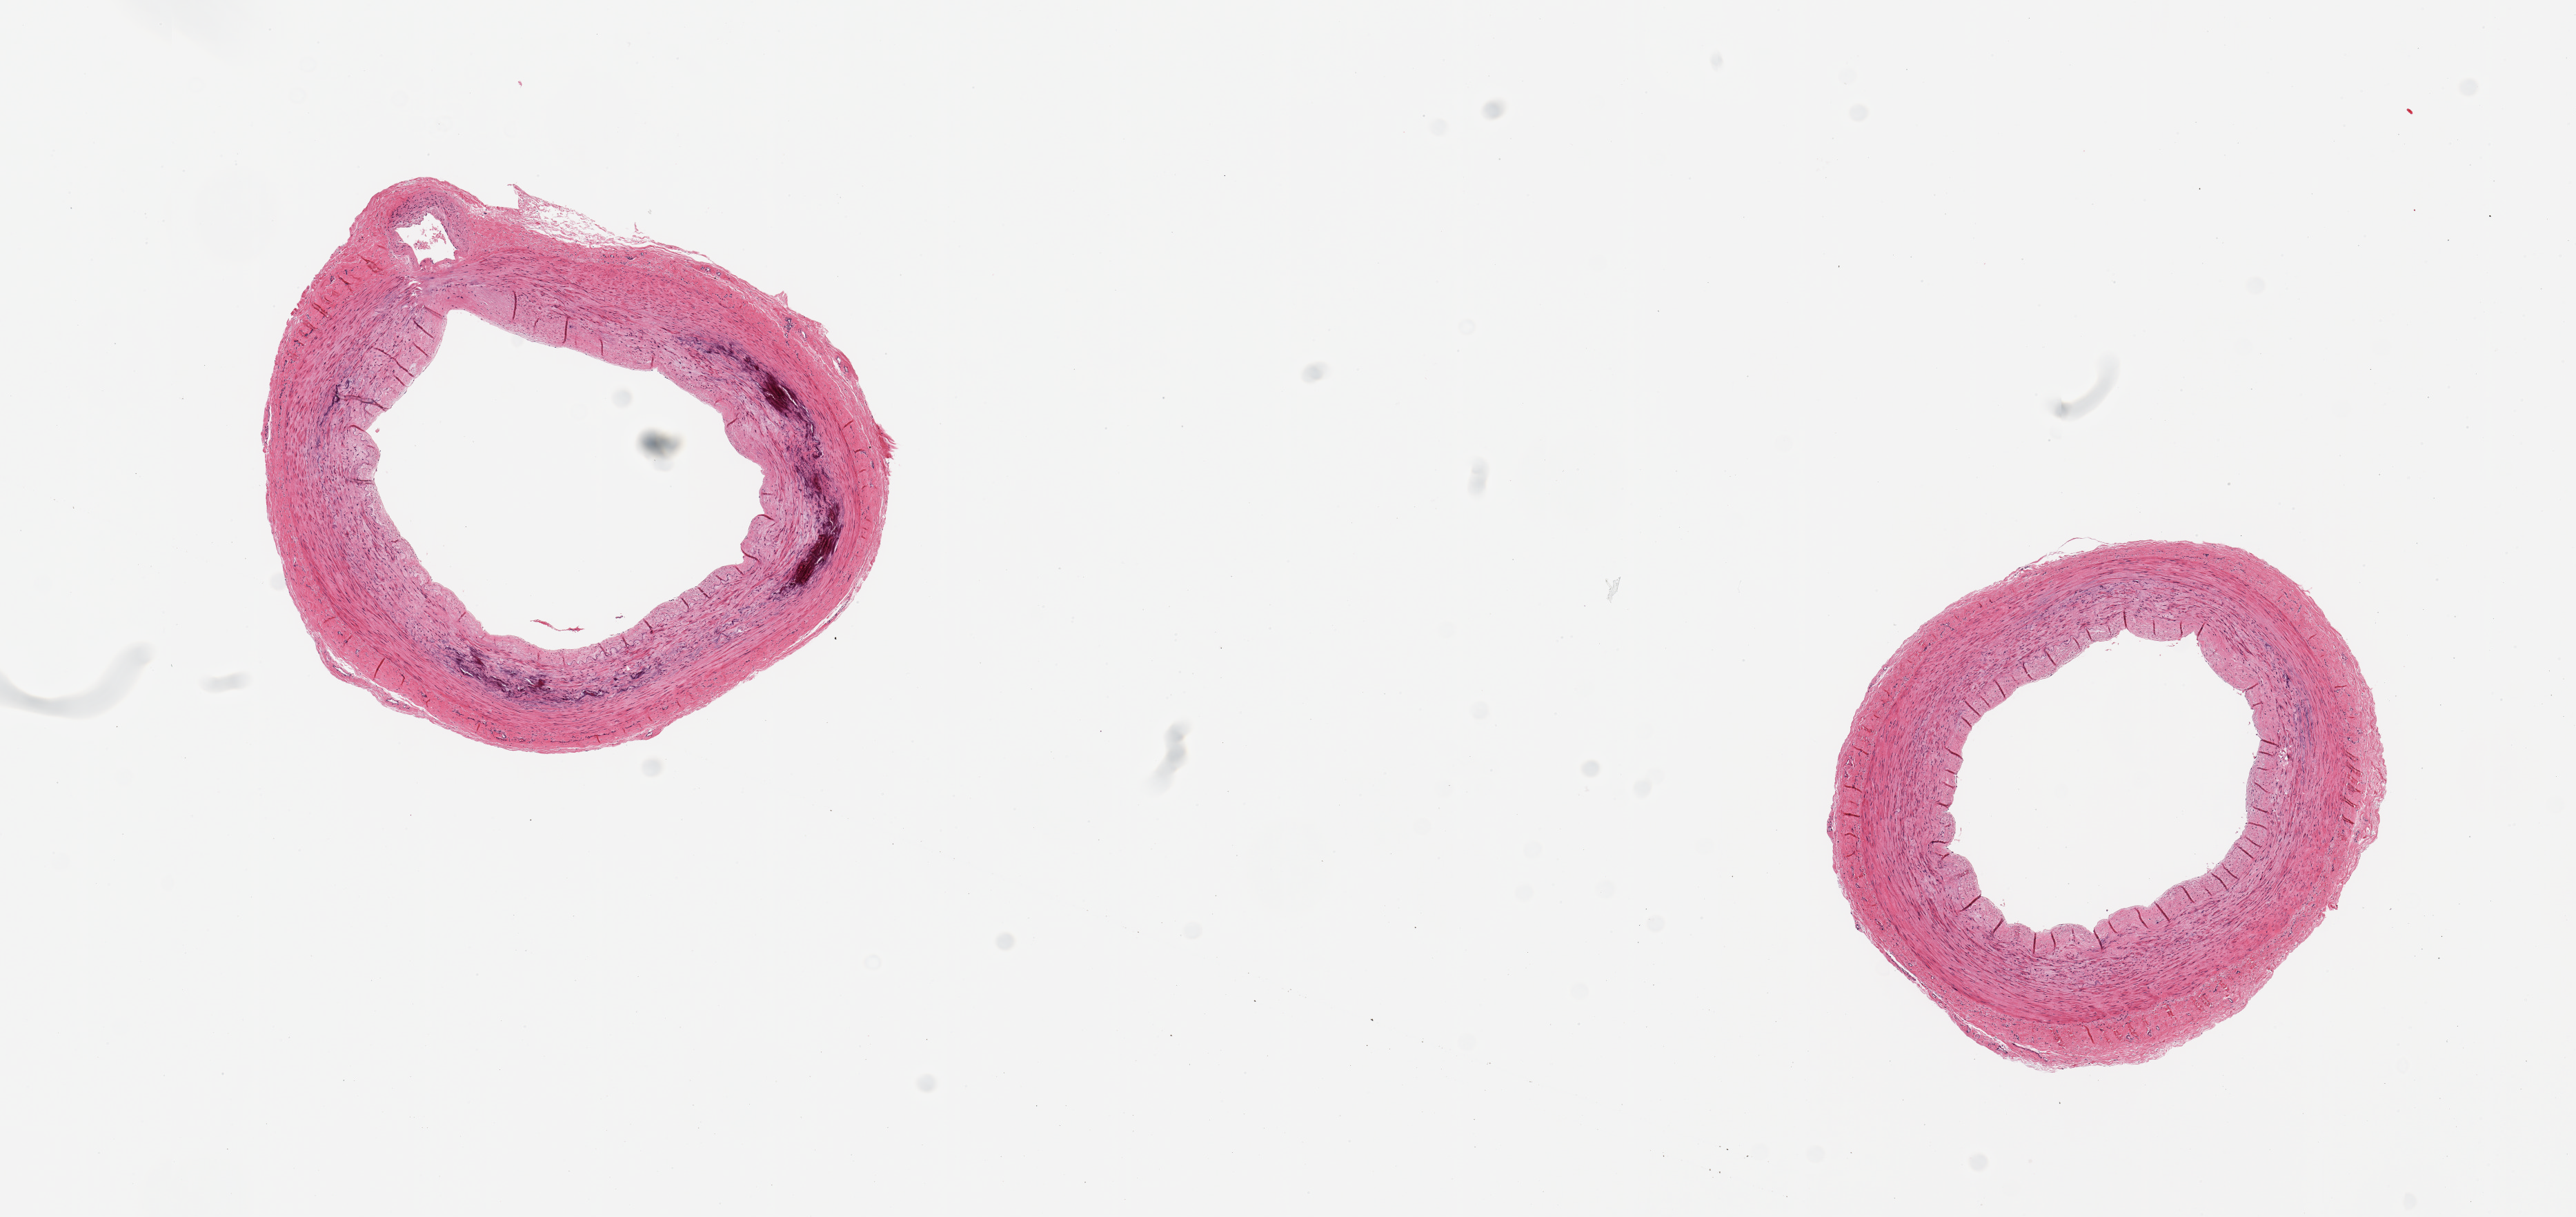
Digitized H&E-stained section, brightfield — shown as a low-resolution overview of the whole scanned area (about 14.8 x 7.0 mm, from a 20x scan). PAXgene-fixed paraffin-embedded (PFPE) section. Sampled site (target tissue): tibial artery. Donor tissue sample.
* review note (as recorded): 2 pieces, no atherosis, focal Monckeberg medial sclerosis